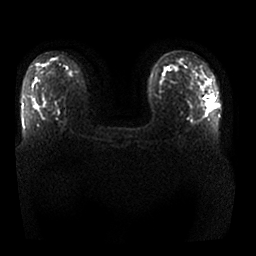
Breast MRI, one axial slice. Position 16 of 25 along the scan axis. Diffusion-weighted series; image 2 of 4 stored at this slice position (different b-values; order by instance number). 1.5 T. 4 mm slice thickness. 256 × 256 image matrix, field of view 360 × 360 mm. Female patient.
Outlined on this slice (manually delineated by an expert):
- tumour on diffusion-weighted imaging: bounding box [x1, y1, x2, y2] px = [207, 96, 213, 108]